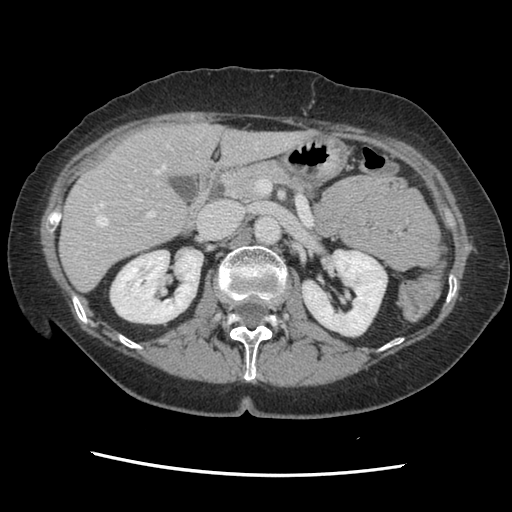
Contrast-enhanced abdominal CT, one axial slice; slice 74 of 141 in the series (ordered by position); 120 kVp; soft-tissue window (W 400 / L 40 HU); 512 × 512 image matrix, field of view 330 × 330 mm. Female patient, age 61 years. From the clinical record (not read from this slice): diagnosis: colorectal cancer liver metastases, imaged before liver resection; multiple liver metastases: no; largest metastasis: 2.4 cm.
Outlined on this slice (manually delineated by an expert):
- hepatic veins: bounding box (x1, y1, x2, y2) in pixels: (85, 142, 259, 267)
- liver: (61, 124, 307, 290)
- planned liver remnant (the part of the liver to remain after resection): (61, 124, 306, 290)
- portal vein (with intrahepatic branches): (93, 185, 155, 244)